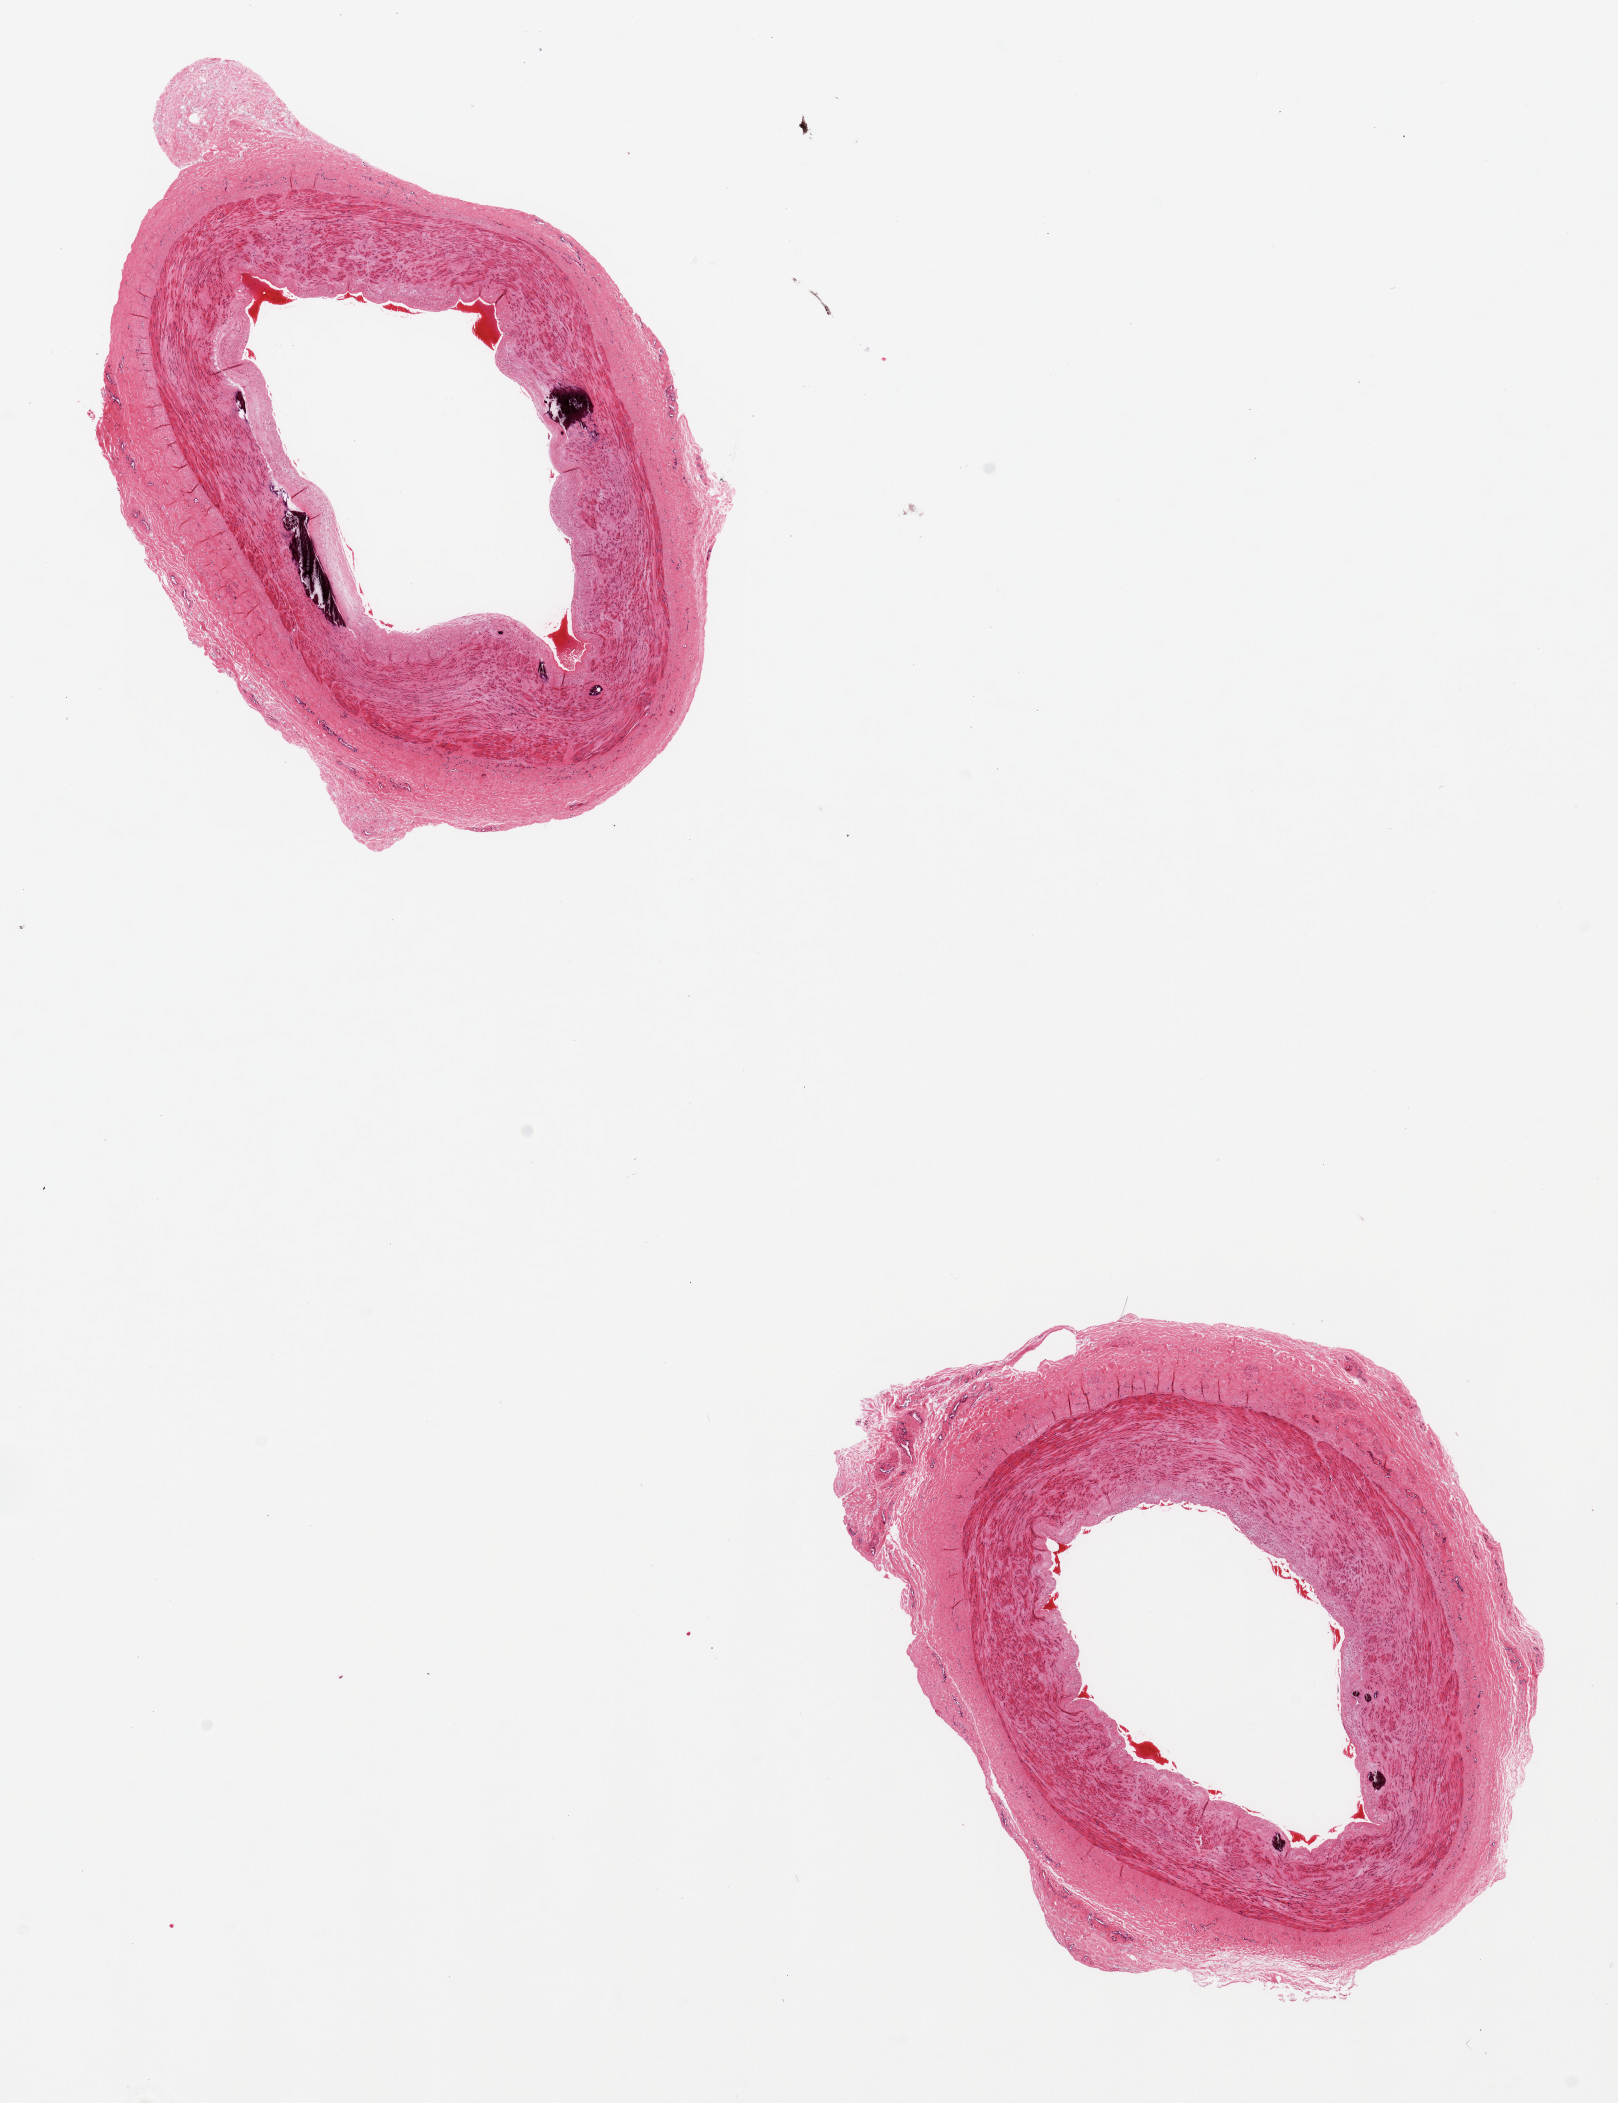
Whole-slide image, hematoxylin and eosin (H&E) stain, a low-resolution overview of the entire scanned area, about 12.8 x 16.6 mm. PAXgene-fixed, paraffin-embedded tissue. Target tissue: tibial artery. Tissue donor sample. Donor sex: male.
- pathologist's review note for this sample: 2 pieces, no adherent fat; trace atherosis; Monckeberg medial sclerosis